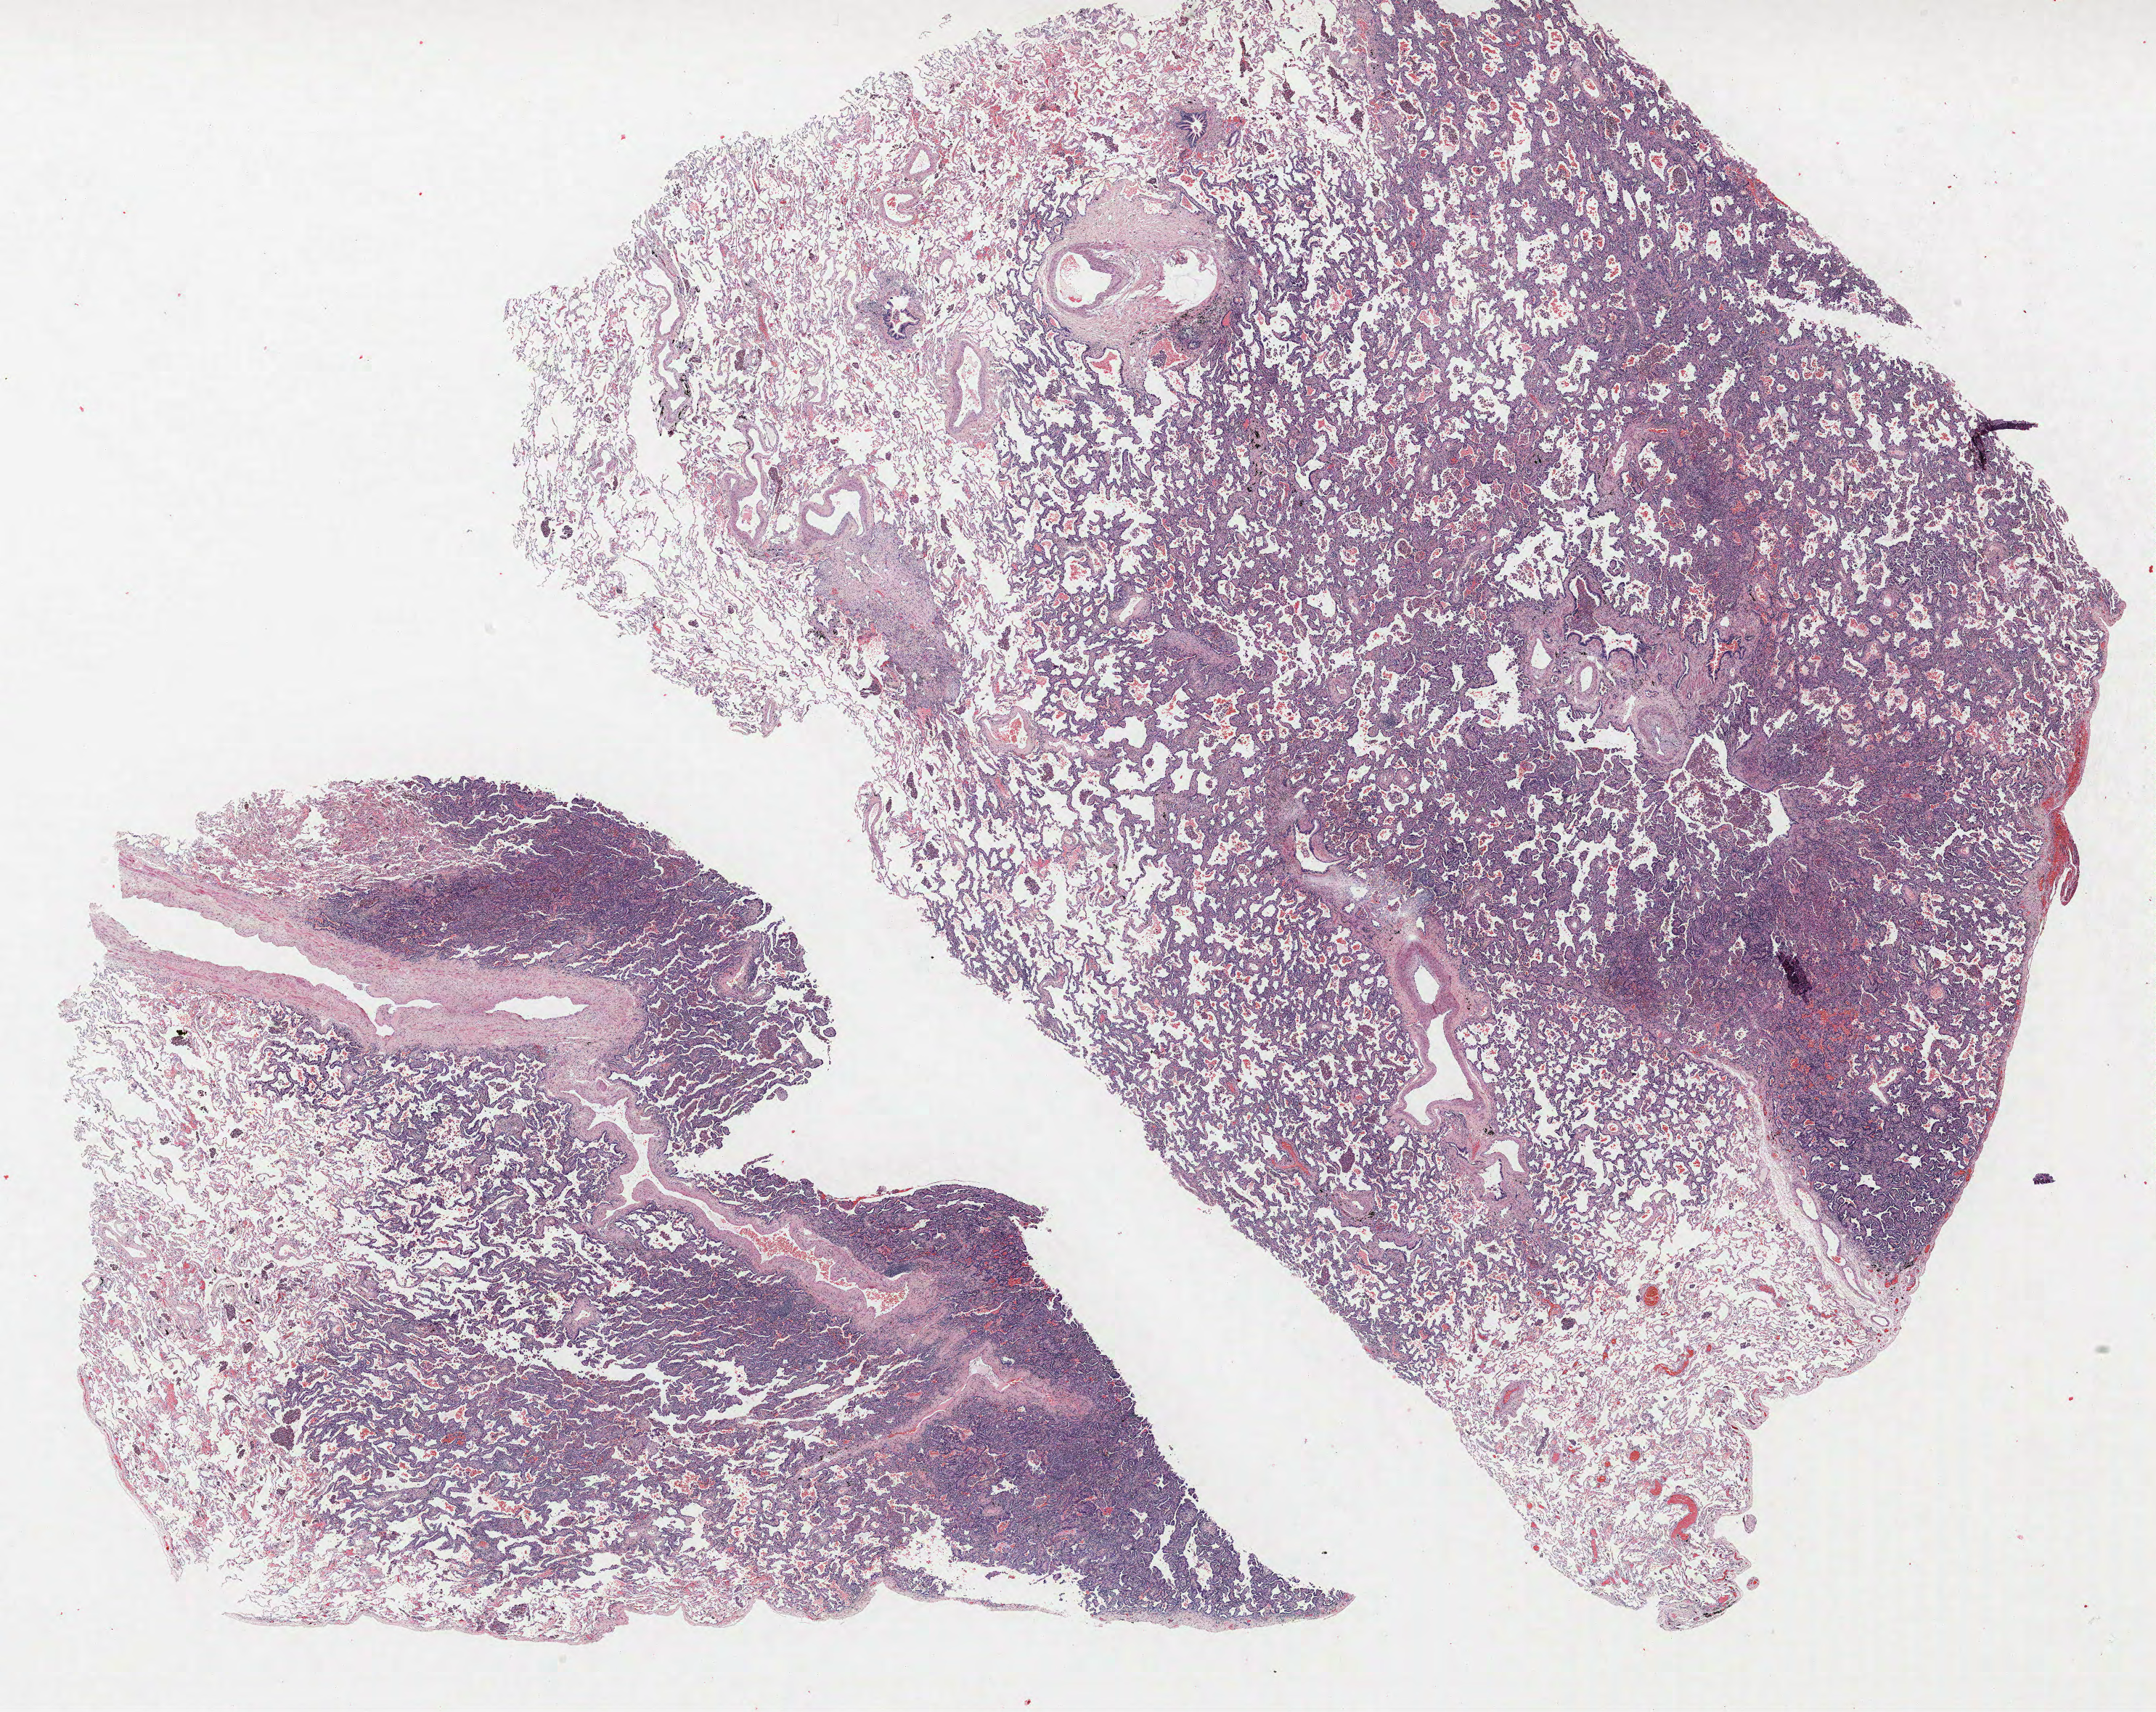
Whole-slide histology image, H&E — whole scanned area (about 23.8 x 18.9 mm, from a 40x scan) shown as a low-resolution overview, FFPE section, lung tissue. Female patient, aged 64 at enrolment. Grade: well differentiated (G1).
Participant's lung-cancer diagnosis: Bronchiolo-alveolar carcinoma, non-mucinous. Stage (AJCC 6th edition): IA. Tumour size (pathology): 20 mm. Primary tumour location (clinical record): right lower lobe. ICD-O-3 topography: lower lobe of lung (C34.3).